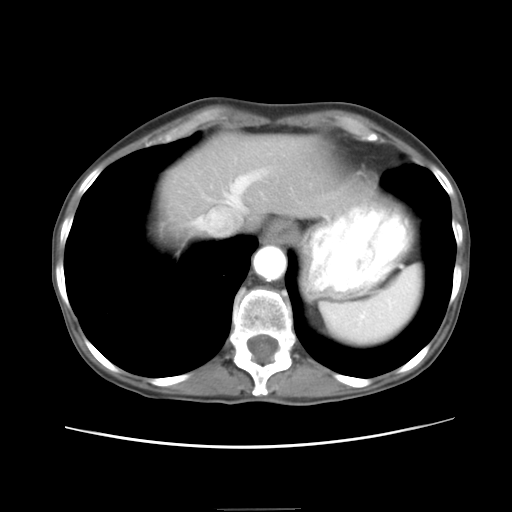
Contrast-enhanced abdominal CT, one axial slice; 120 kVp; intravenous contrast given; soft-tissue window (W 400 / L 40 HU); 512 × 512 image matrix, field of view 340 × 340 mm. Female patient, age 65 years. From the clinical record (not read from this slice): diagnosis: colorectal cancer liver metastases, imaged before liver resection; multiple liver metastases: no.
Annotated regions visible in this slice (manually delineated by an expert):
- hepatic veins: bounding box [x1, y1, x2, y2] px = [195, 171, 263, 223]
- liver: [157, 141, 348, 237]
- planned liver remnant (the part of the liver to remain after resection): [157, 141, 348, 238]